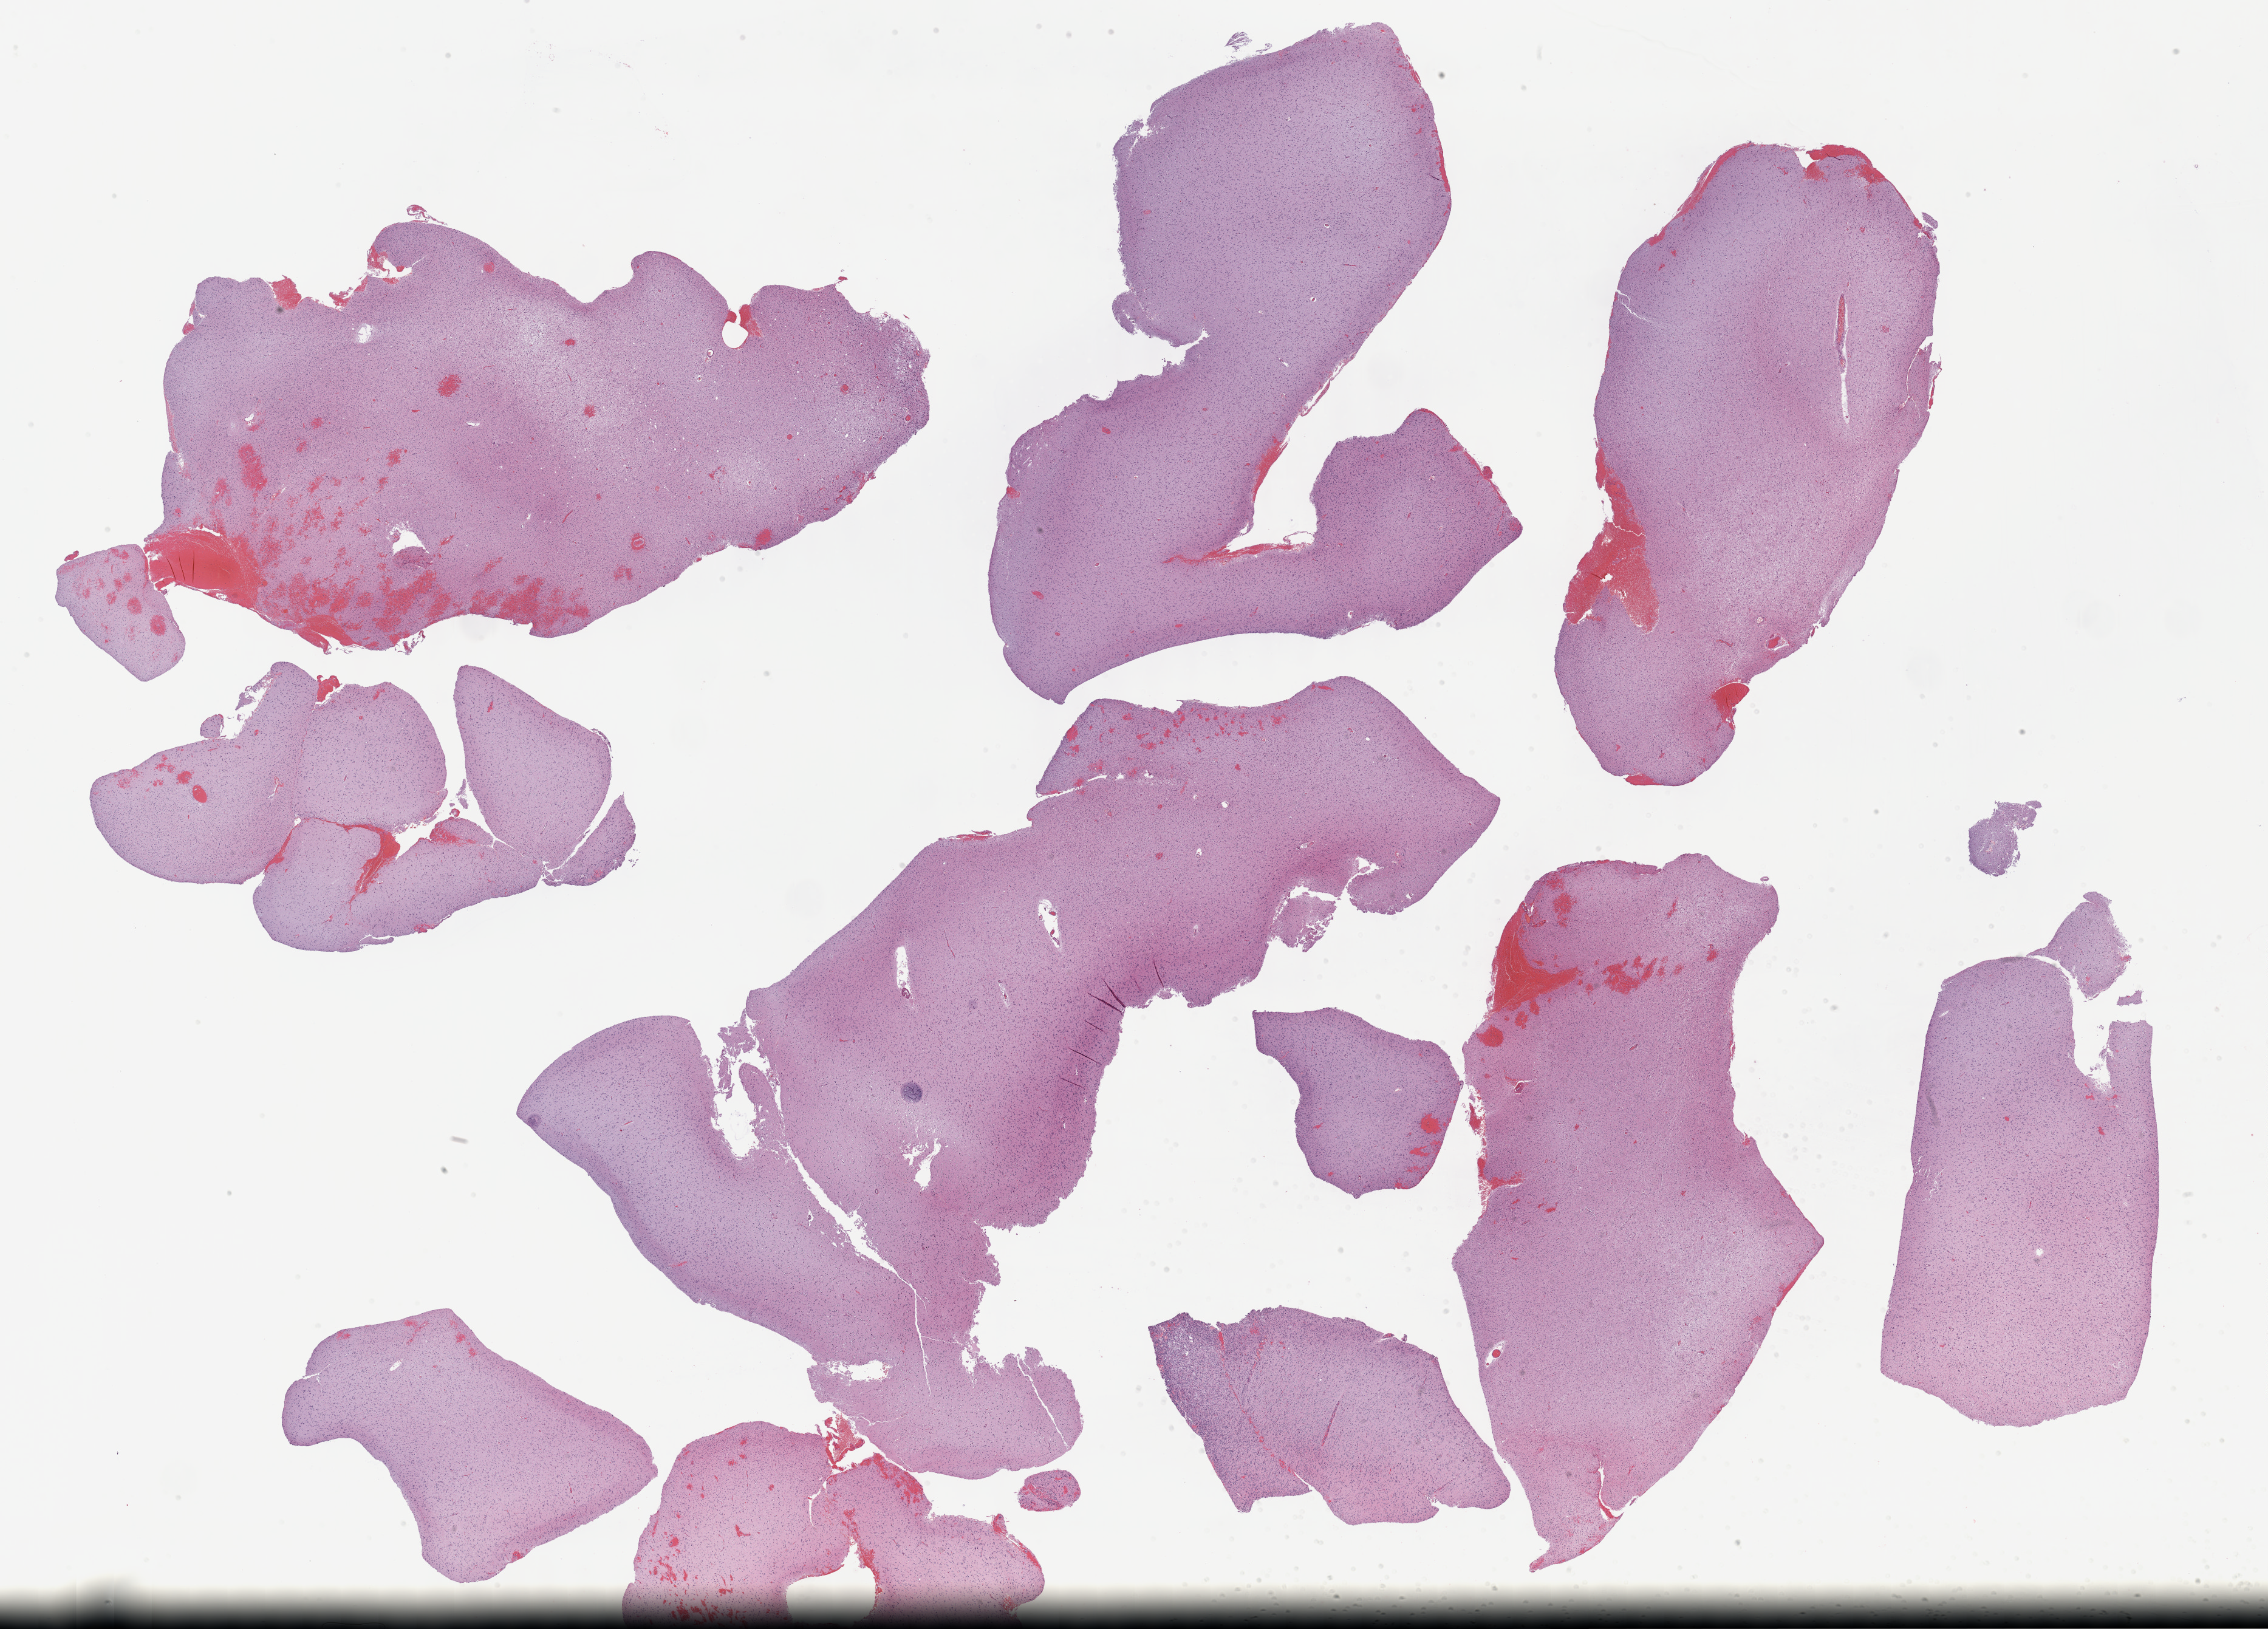
H&E whole-slide image — shown as a low-resolution overview of the whole scanned area (about 30.2 x 21.7 mm); formalin-fixed paraffin-embedded (FFPE) diagnostic section; sample: primary tumour, brain. Patient: male, age at initial diagnosis 54 years. Histologic grade: G2 (moderately differentiated).
* histologic diagnosis: Oligodendroglioma, NOS (cerebrum)